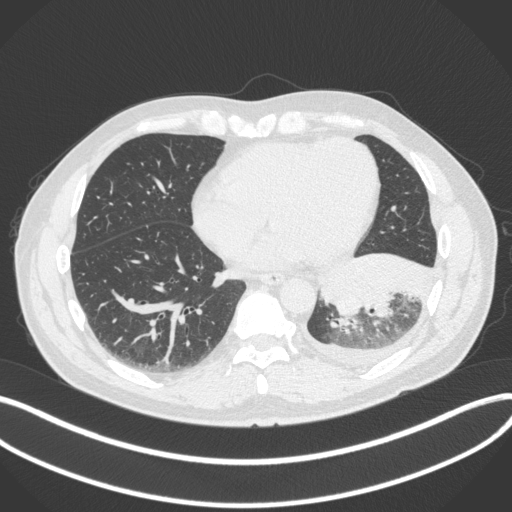
Chest CT, one axial slice. Slice 123 of 350 in the series (ordered by position). Reconstruction kernel B31f. 120 kVp. Lung window (W 1500 / L -600 HU). 512 × 512 image matrix. Male patient, age 58 years. Case-level facts recorded for this patient, not image findings: clinical TNM (as recorded): T3 N1 M1b; histopathological grade: G3.
Outlined on this slice (bounding box drawn by a radiologist):
- lung tumour (recorded histology: small cell carcinoma): bounding box <316,252,437,318> (left, top, right, bottom; pixels)